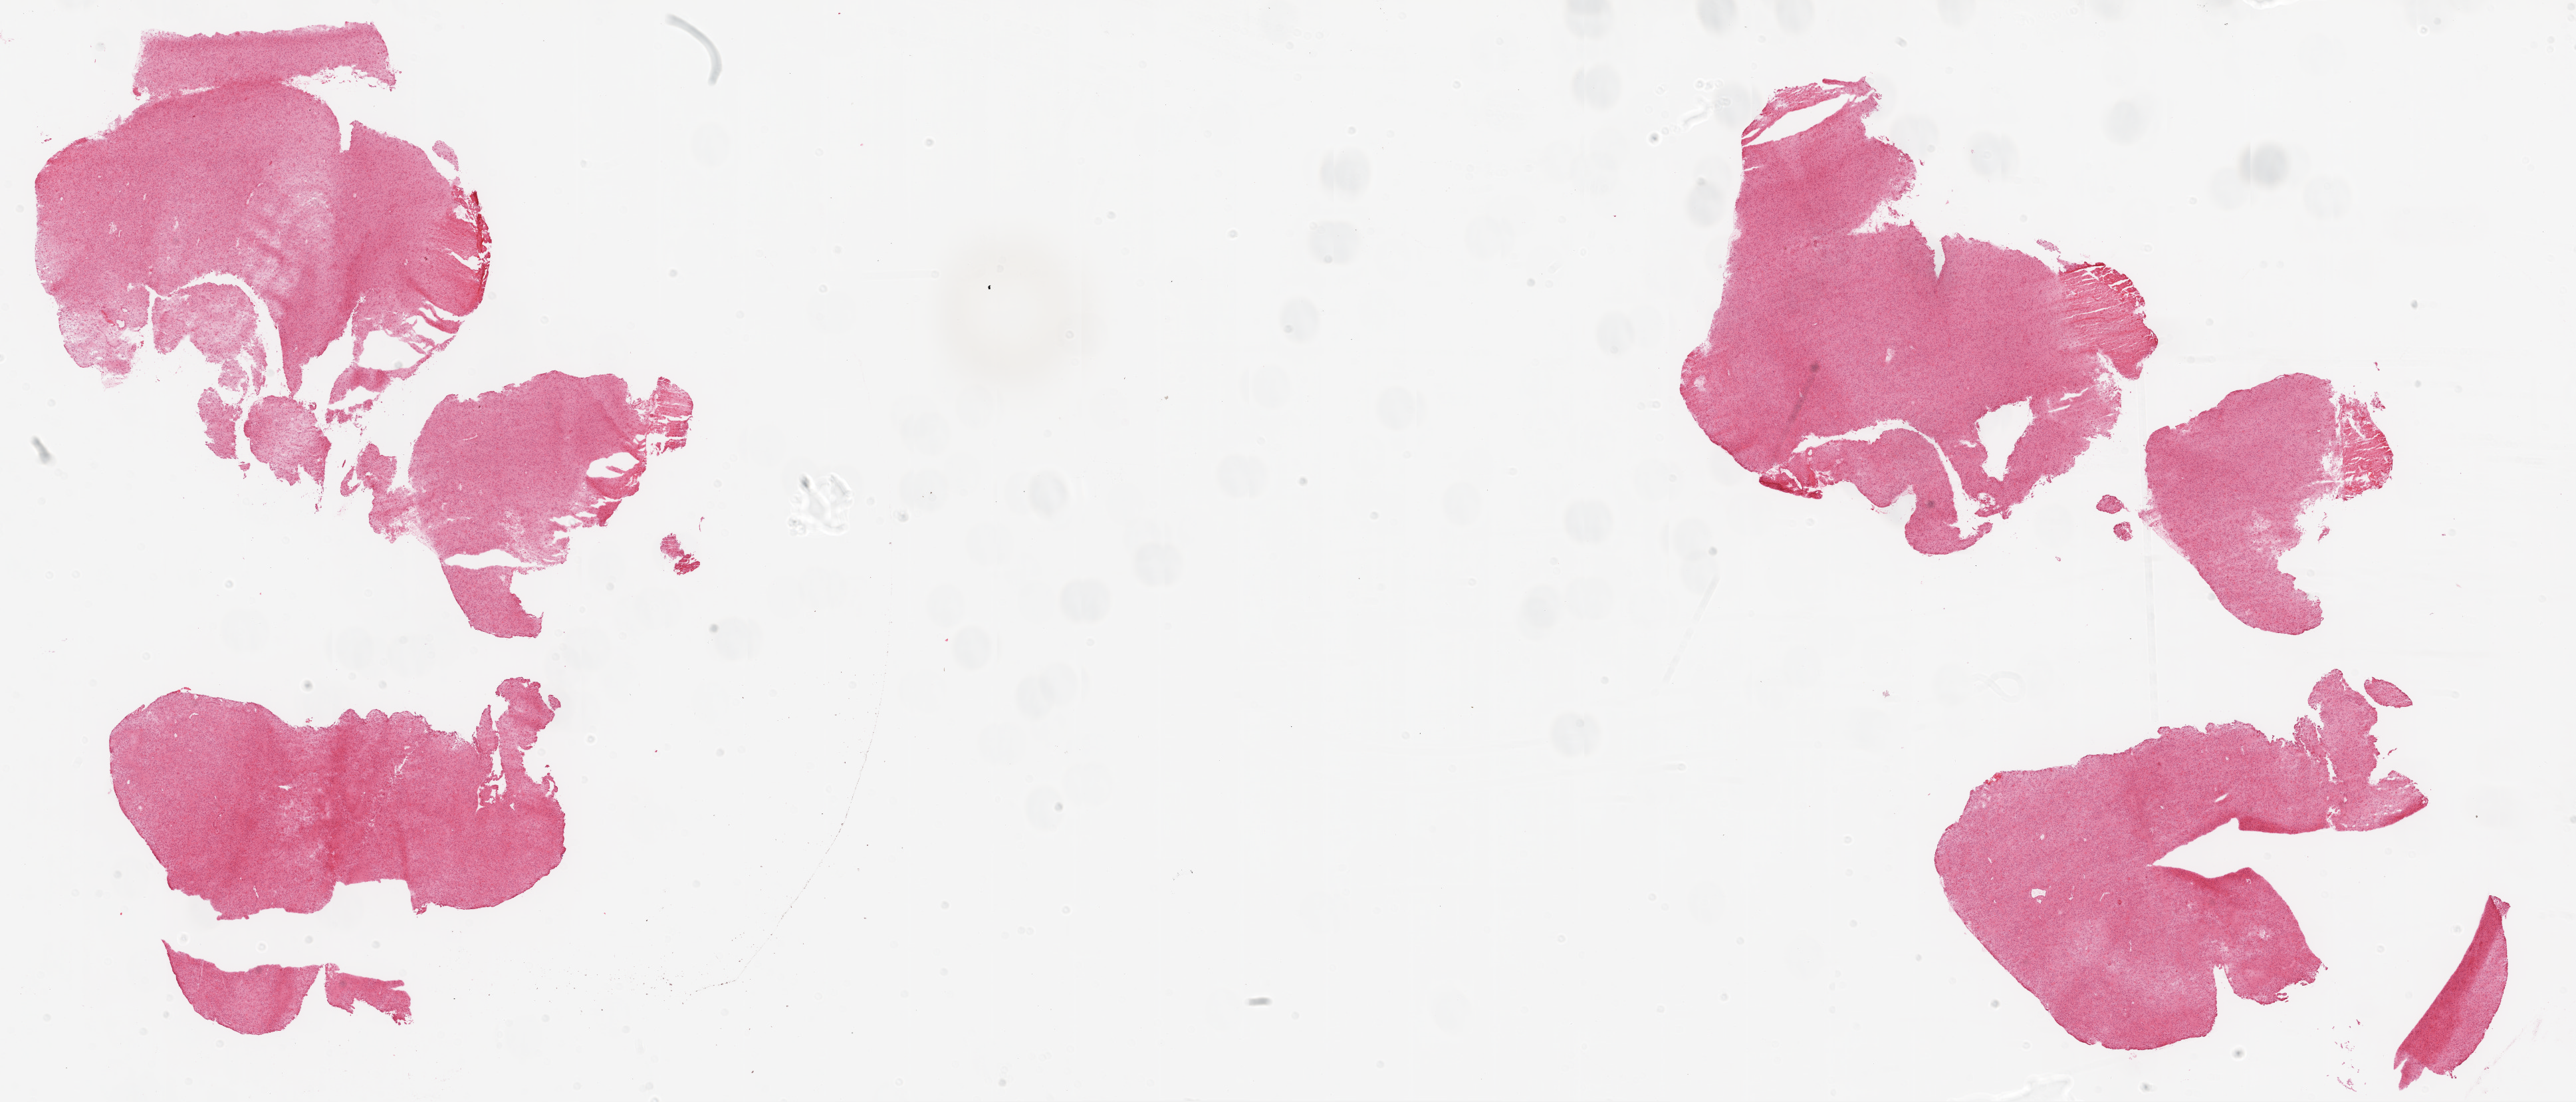
Whole-slide histology image, H&E-stained — whole scanned area (about 31.1 x 13.3 mm, slide scanned at 20x) shown as a low-resolution overview, frozen section from the top of the tissue portion, sample: primary tumour, brain. Patient: male, age at initial diagnosis 36 years. Pathologist review of this section (percent, as recorded): tumour cells 90%, tumour nuclei 85%, normal cells 0%, stromal cells 5%, necrosis 5%.
Pathologic diagnosis: Glioblastoma.